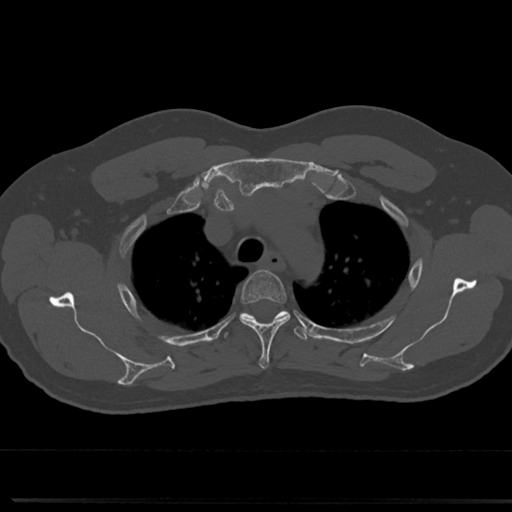
CT including the spine, one axial slice; reconstruction kernel Br40s/3; 120 kVp; bone window (W 1800 / L 400 HU); 512 × 512 image matrix. Patient: male, 61 years. From the clinical record (not read from this slice): primary cancer: prostate.
Annotated regions visible in this slice (semi-automatic segmentation, software-assisted and operator-edited):
- T3 vertebra: bounding box [x1, y1, x2, y2] px = [239, 271, 290, 370]
- T4 vertebra: [221, 309, 309, 344]